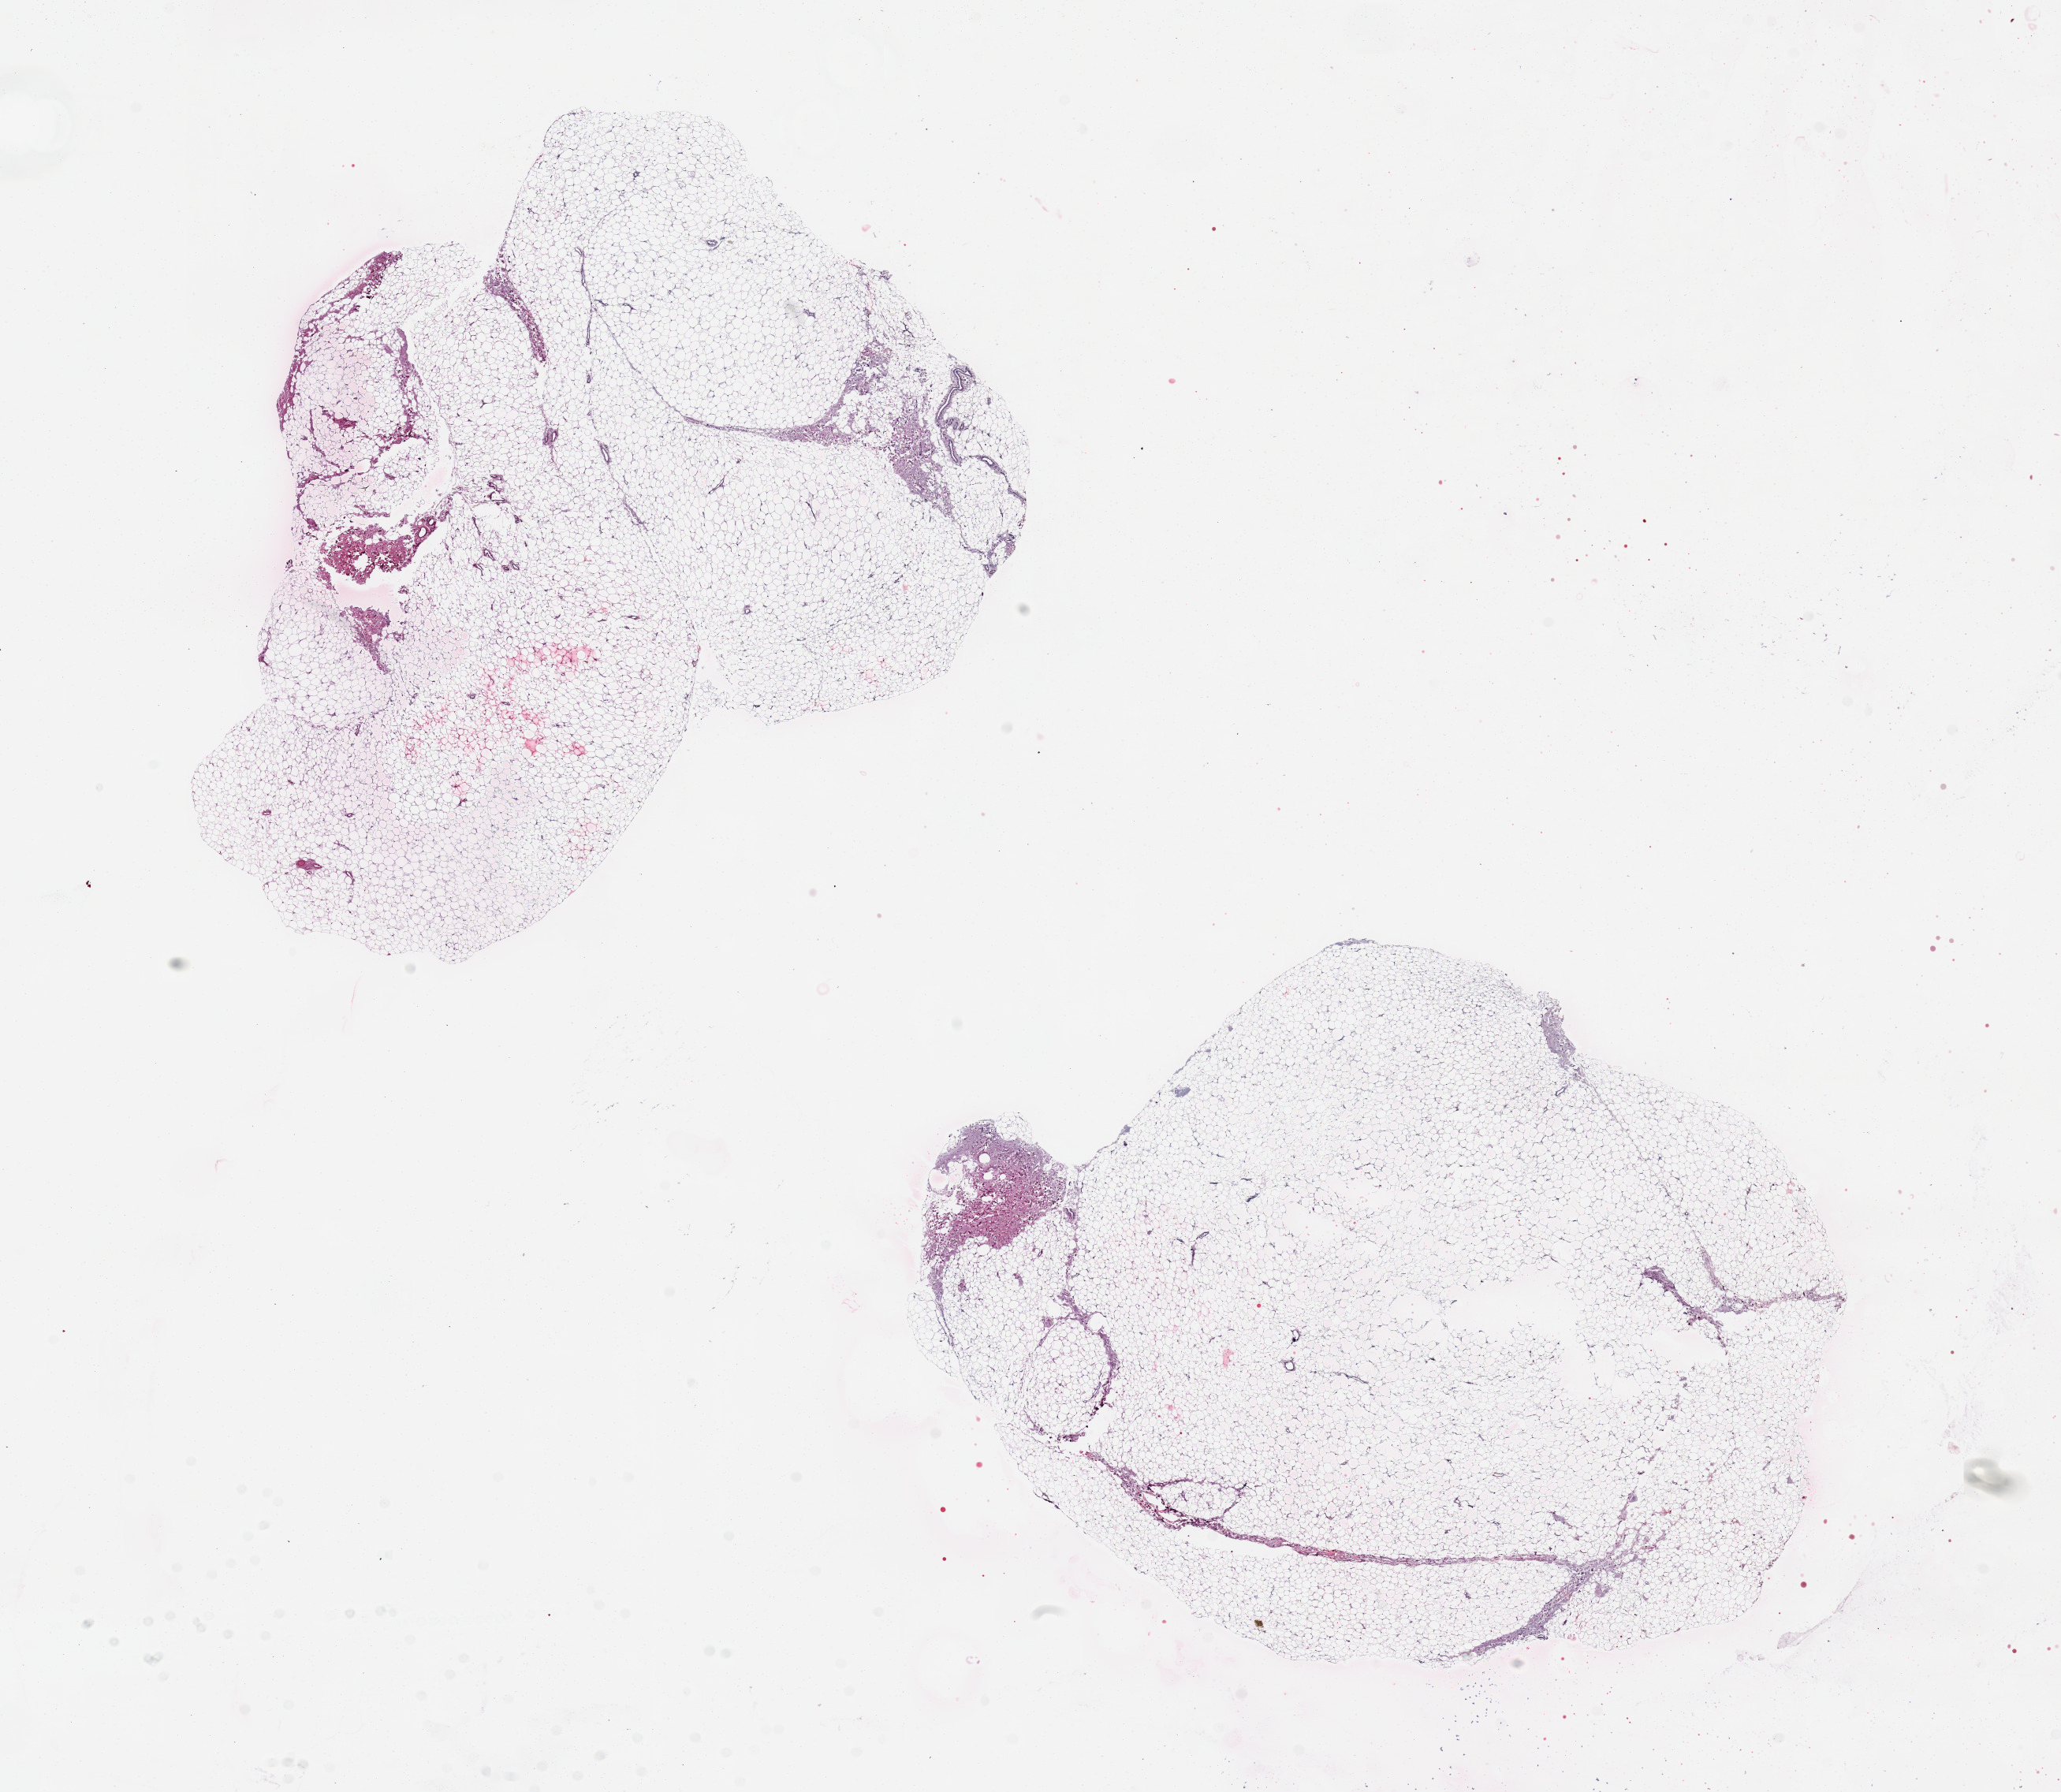
Whole-slide image, H&E stain, a low-resolution overview of the entire scanned area, about 20.7 x 18.0 mm (from a 20x scan). PAXgene-fixed paraffin-embedded (PFPE) section. Section of breast (target tissue). Tissue donor sample. Donor: male.
• review note (as recorded): 2 pieces, 8x7 & 9x6 mm; all adipose, no mammary tissue